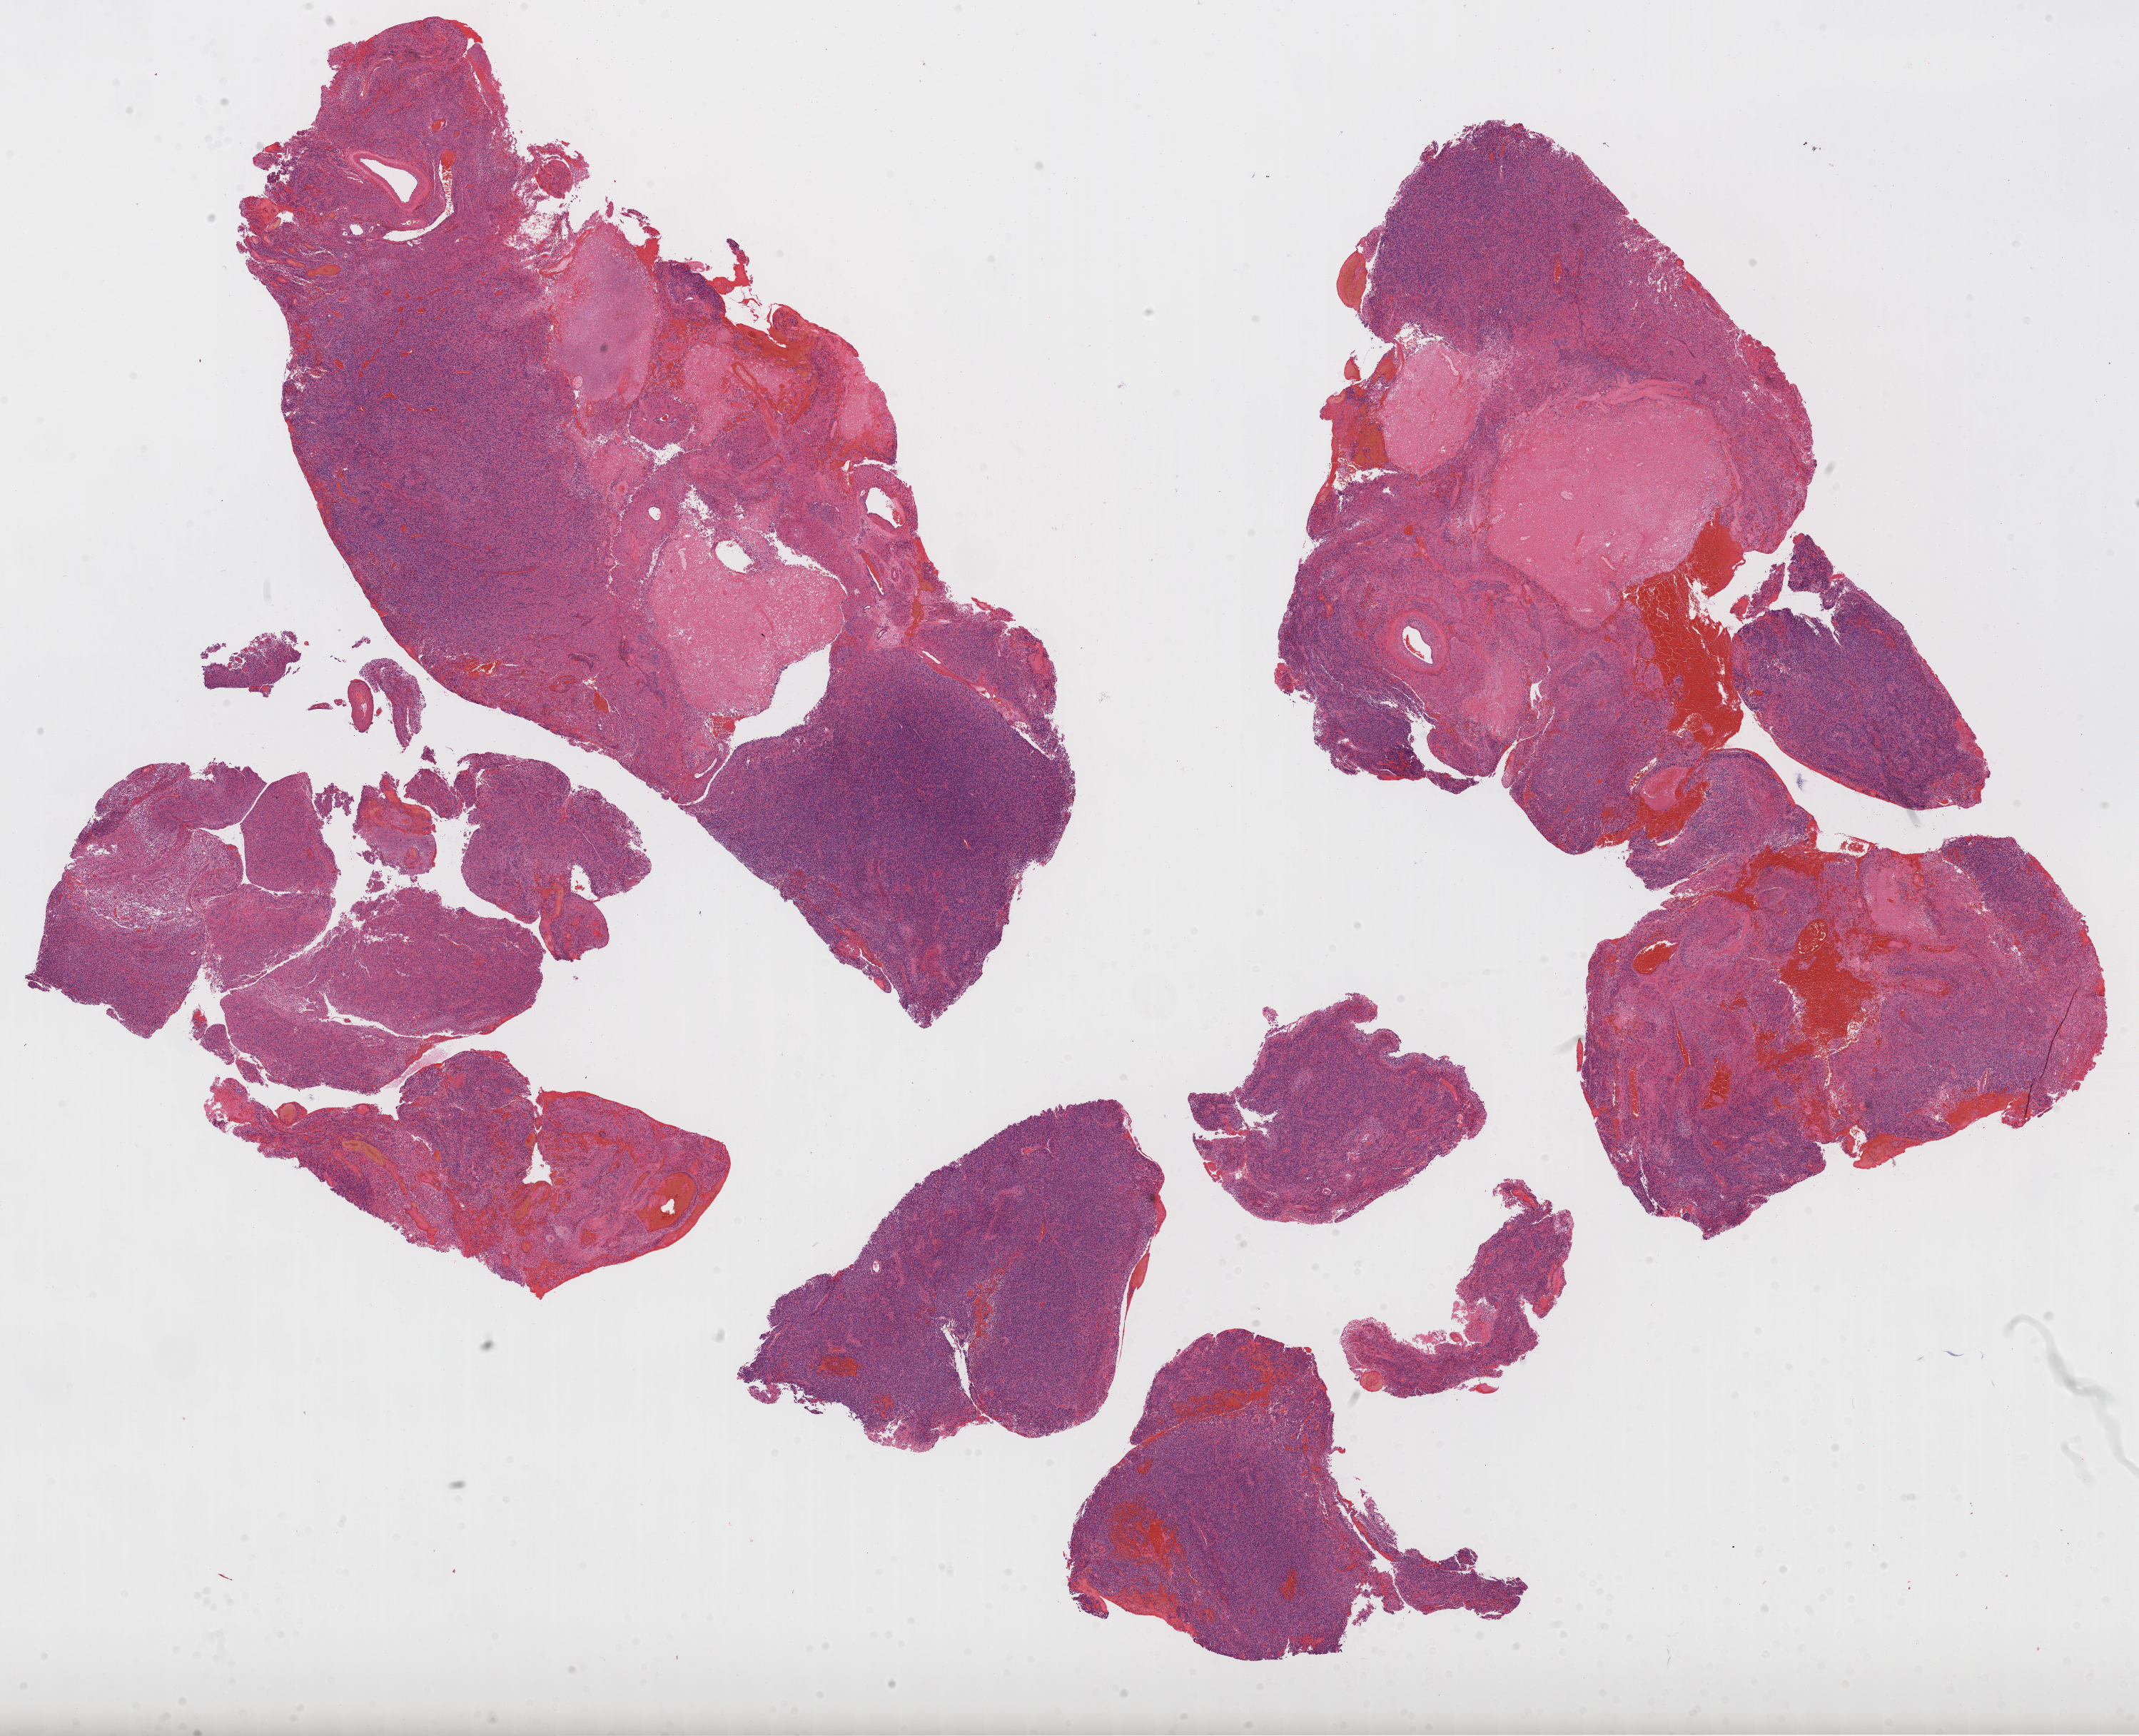
Whole-slide histology image, Hematoxylin and eosin (H&E) stained, low-resolution overview of the scanned area, about 24.2 x 19.6 mm (slide scanned at 20x). Formalin-fixed paraffin-embedded (FFPE) diagnostic section. Brain, primary tumour sample. Female, age 61 years at initial diagnosis.
• diagnosis: Glioblastoma